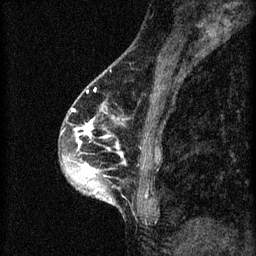
Breast MRI (dynamic contrast-enhanced), one sagittal slice; slice 24 of 60 in the series (ordered by position); 3 images stored at this slice position (order not interpretable as contrast timing); 1.5 T; TE 4.2 ms, TR 8.2 ms; 2 mm slice thickness; 256 × 256 image matrix. Female patient, age 45 years.
Structures marked on this image (semi-automatically segmented with operator editing):
- analysis volume of interest (the breast-tissue region the enhancement analysis was run in; not a lesion): bounding box (x1, y1, x2, y2) in pixels: (60, 104, 157, 217)
- tumour enhancement mask (voxels above the 70 % enhancement threshold inside the analysis volume of interest): (72, 104, 123, 201)